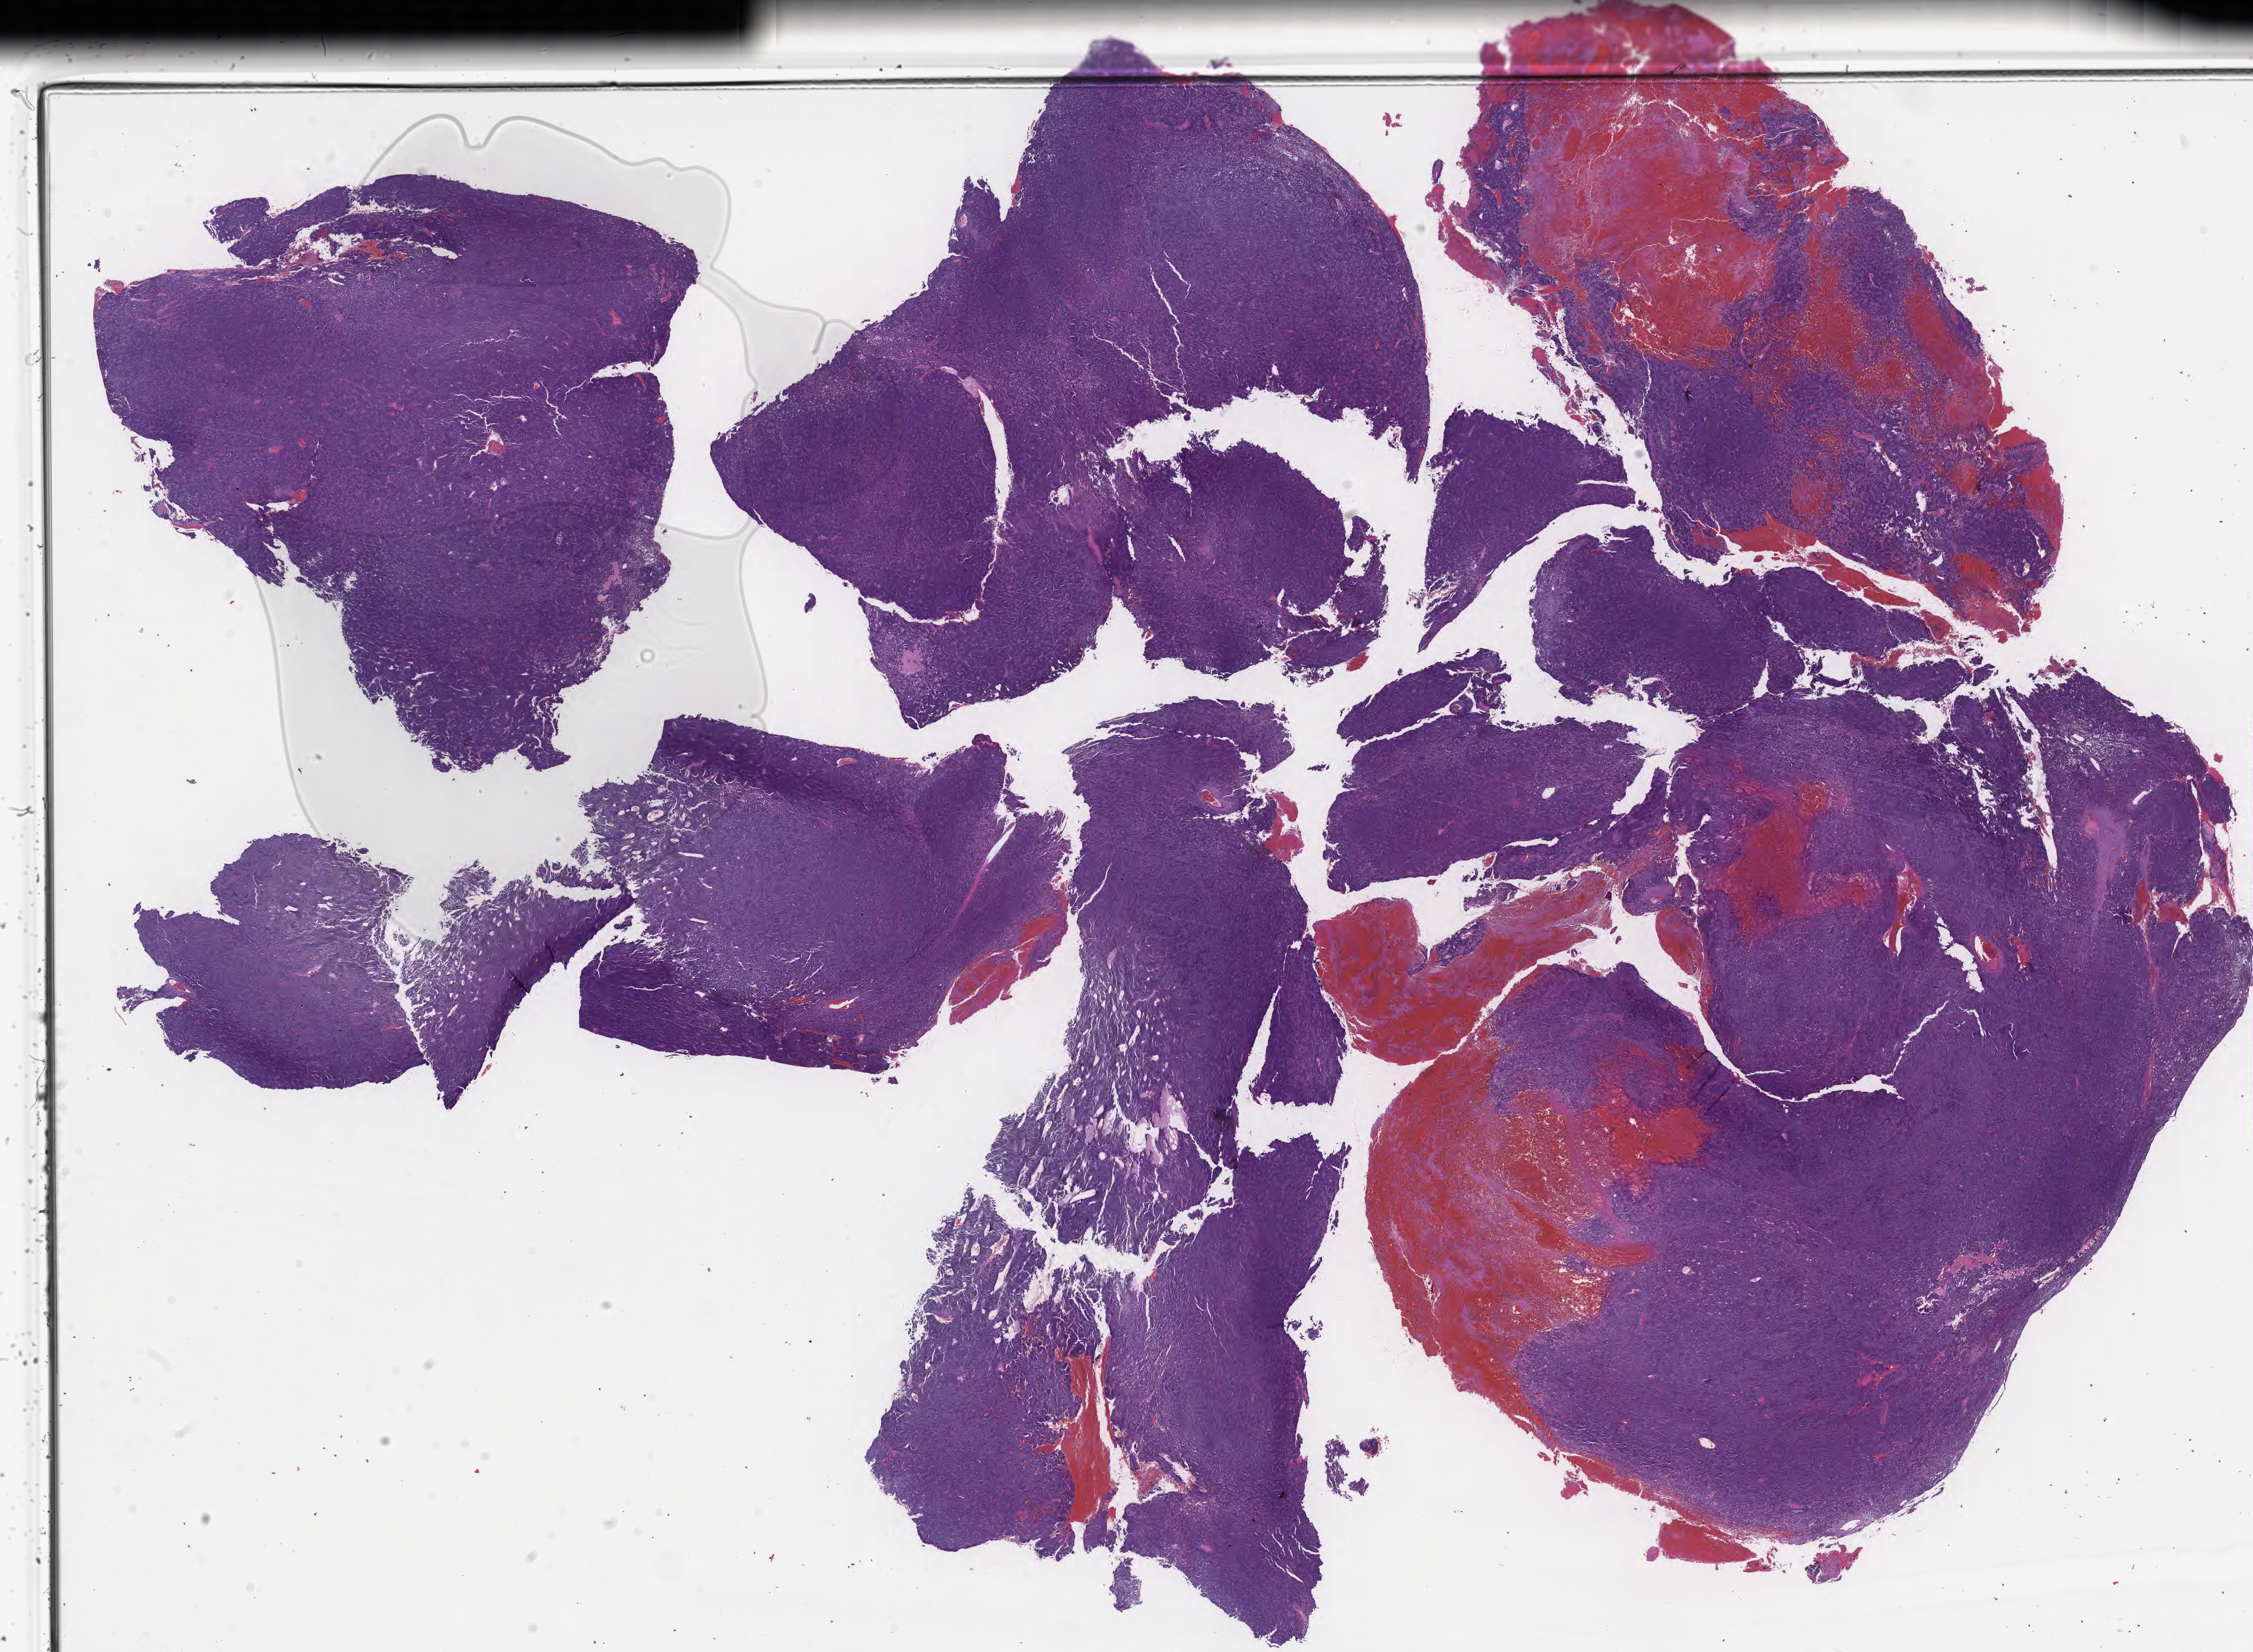
Haematoxylin and eosin whole-slide image of tumor tissue from the soft tissue of lower extremity, shown as a low-resolution overview of the whole scanned area (about 30.7 x 22.5 mm); formalin-fixed, paraffin-embedded (FFPE) tissue. Male patient, age 212 months.
Diagnosis: Spindle cell sarcoma.